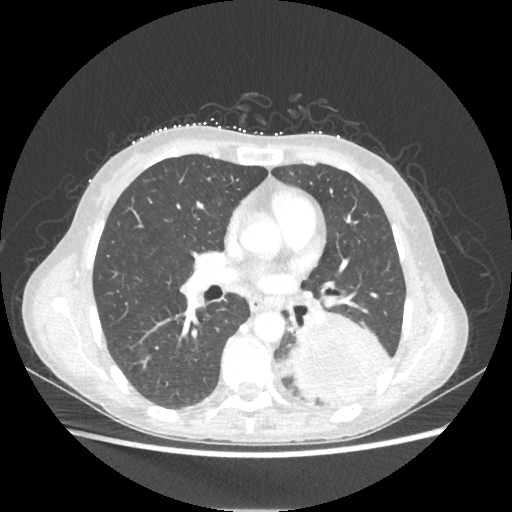
Chest CT, one axial slice; position 115 of 221 along the scan axis; lung window (W 1500 / L -600 HU); 1.25 mm slice thickness; 512 × 512 image matrix. Patient: female, 53 years. Case-level facts recorded for this patient, not image findings: clinical TNM (as recorded): T3 N0 M0.
Annotated regions visible in this slice (rectangle marked by the reading radiologist):
- lung tumour (recorded histology: adenocarcinoma): bounding box (x1, y1, x2, y2) in pixels: (292, 310, 389, 403)